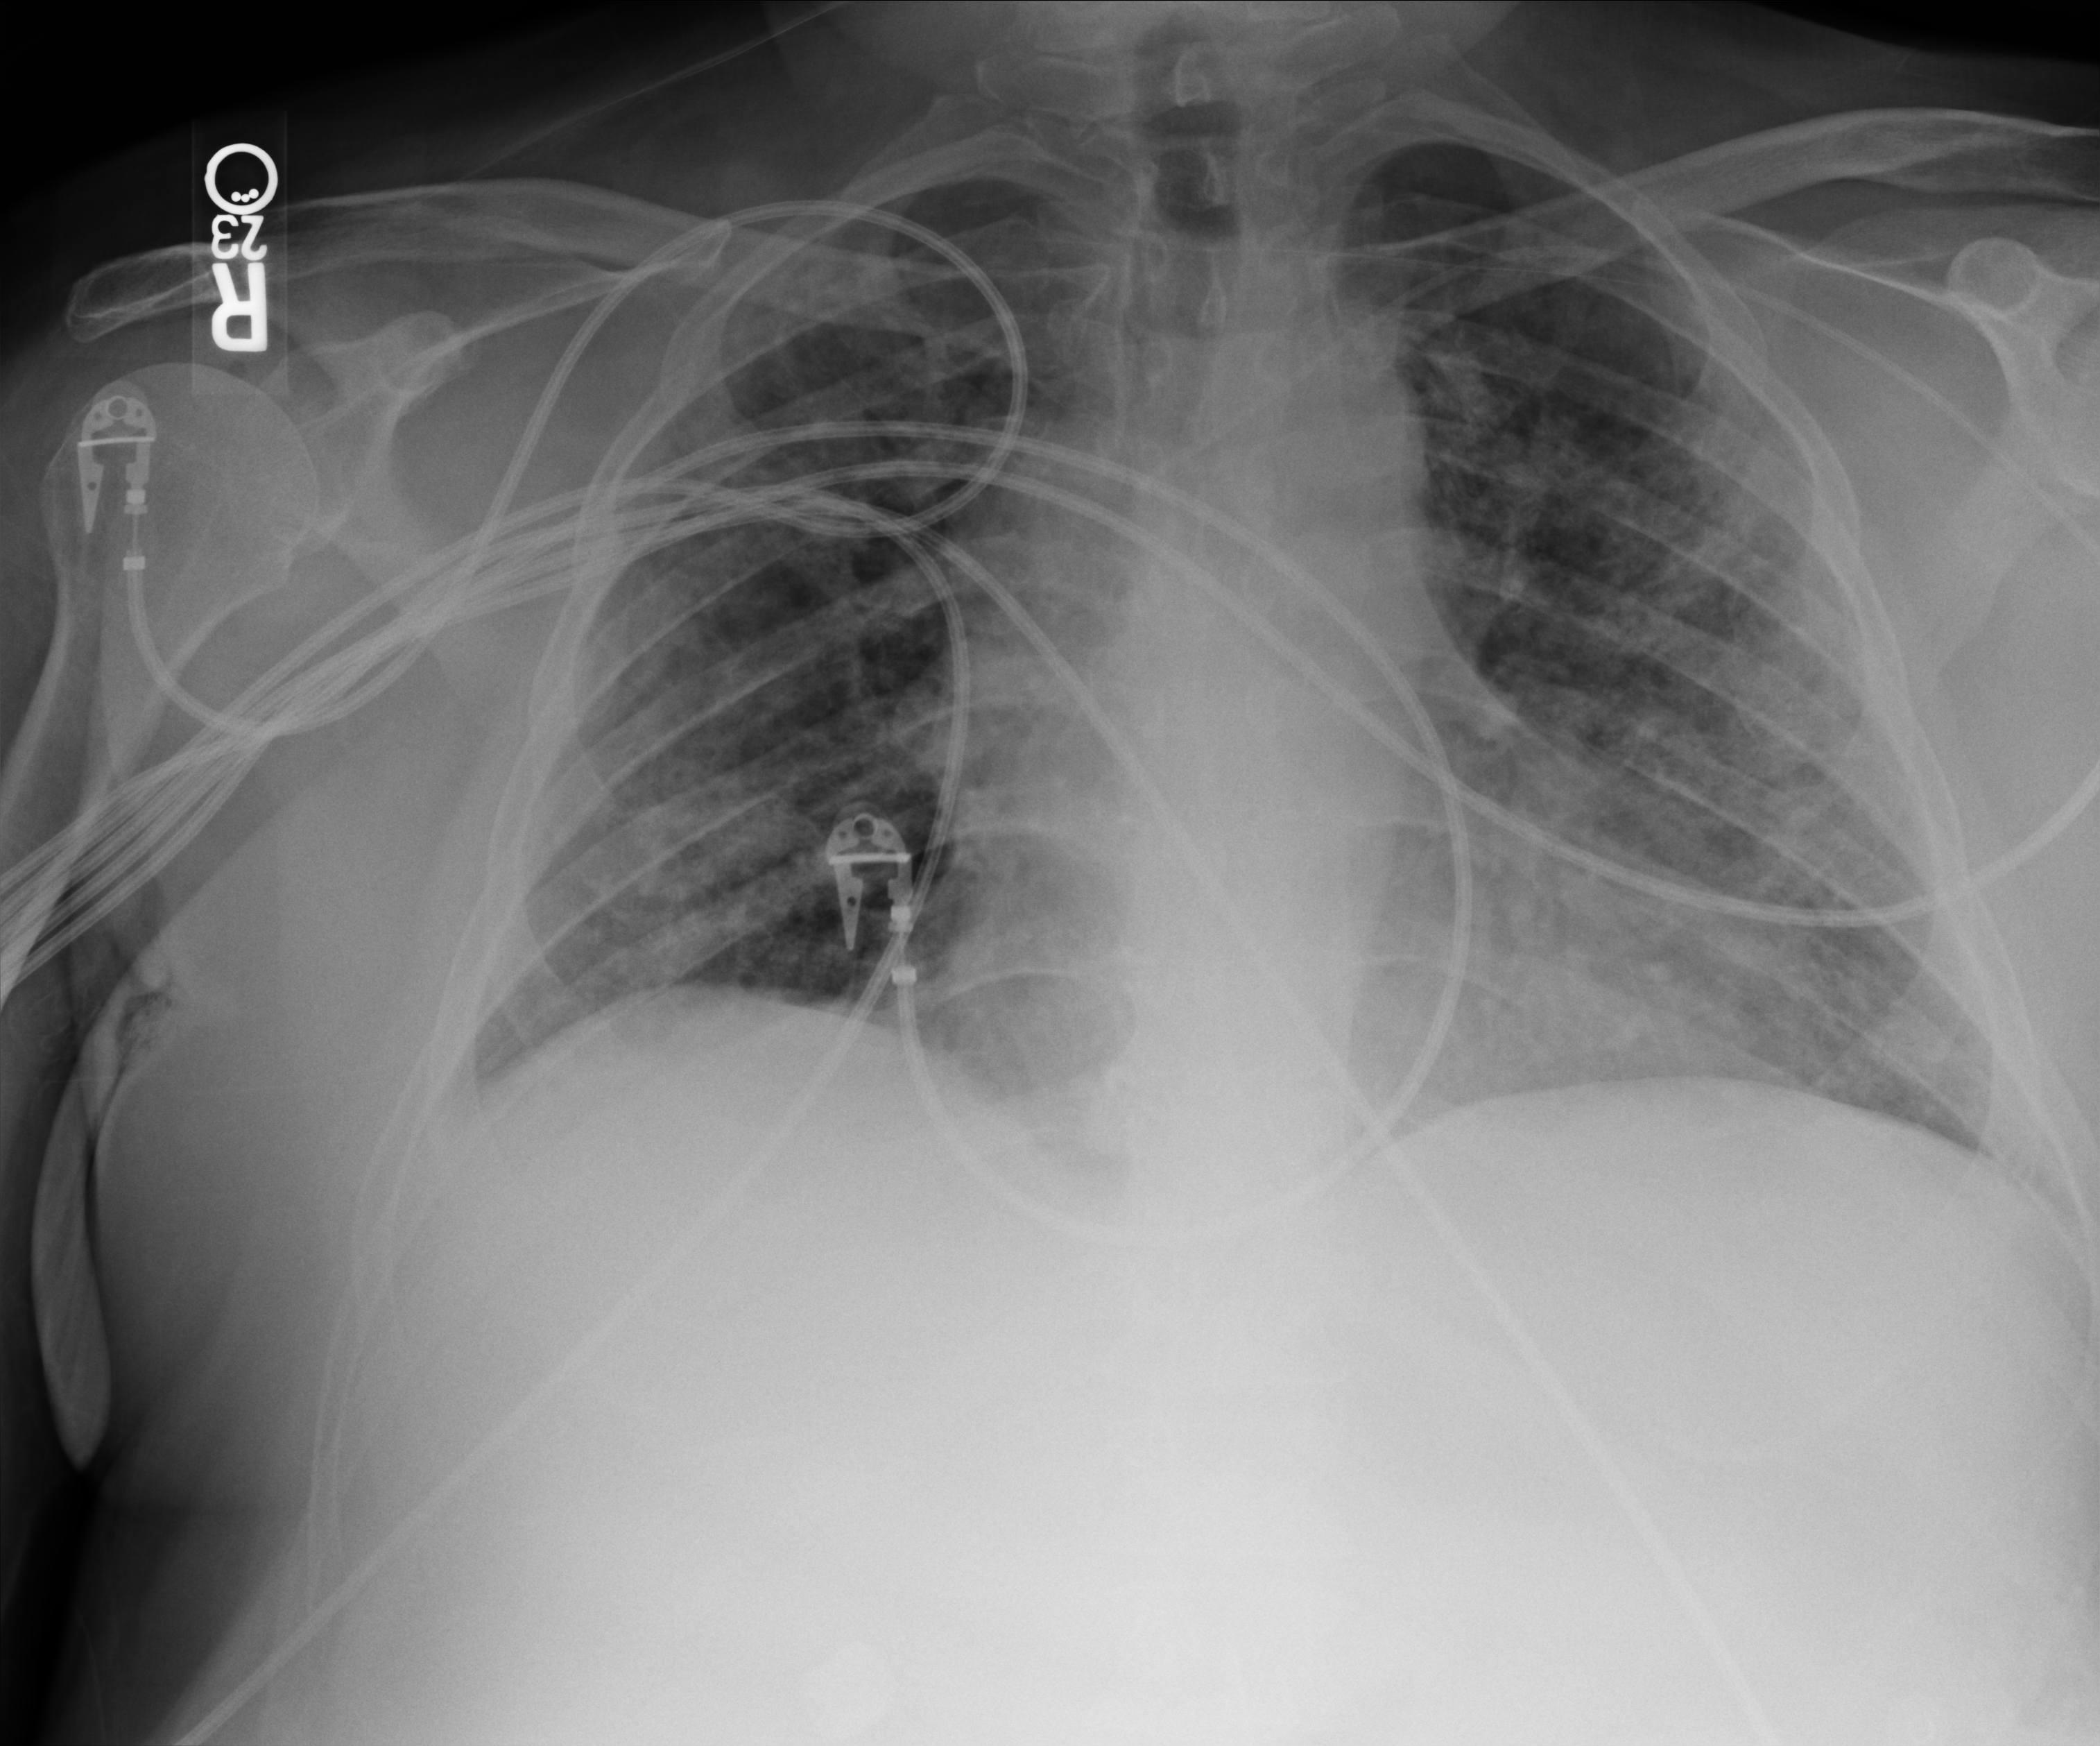
Chest X-ray (portable). Patient hospitalised with COVID-19; male, aged 18–59 years.
Hospital-stay facts (about this admission, not read from this image; timing relative to this image not recorded): mechanically ventilated during this hospital stay: yes; diabetes (admission record): no.